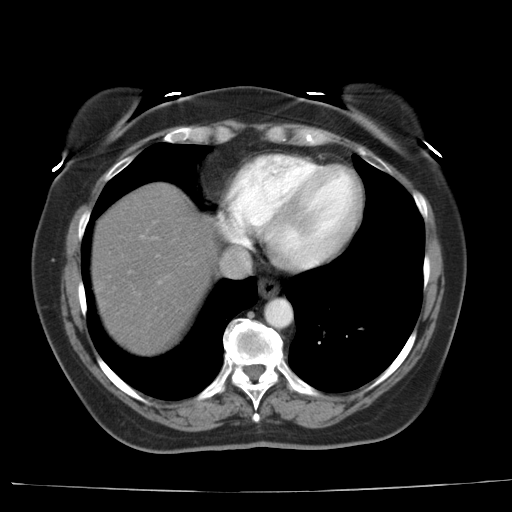
Contrast-enhanced abdominal CT, one axial slice. Slice 34 of 44 in the series (ordered by position). Reconstruction kernel AA-1. 140 kVp. Intravenous contrast given. Soft-tissue window (W 400 / L 40 HU). 5 mm slice thickness. 512 × 512 image matrix, field of view 373 × 373 mm. Female patient. Case-level facts recorded for this patient, not image findings: diagnosis: colorectal cancer liver metastases, imaged before liver resection; multiple liver metastases: yes; largest metastasis: 1.8 cm; disease in both lobes: no.
Annotated regions visible in this slice (outlined manually by an expert reader):
- liver: bounding box (x1, y1, x2, y2) in pixels: (91, 184, 218, 354)
- planned liver remnant (the part of the liver to remain after resection): (127, 184, 218, 264)
- portal vein (with intrahepatic branches): (141, 236, 143, 239)